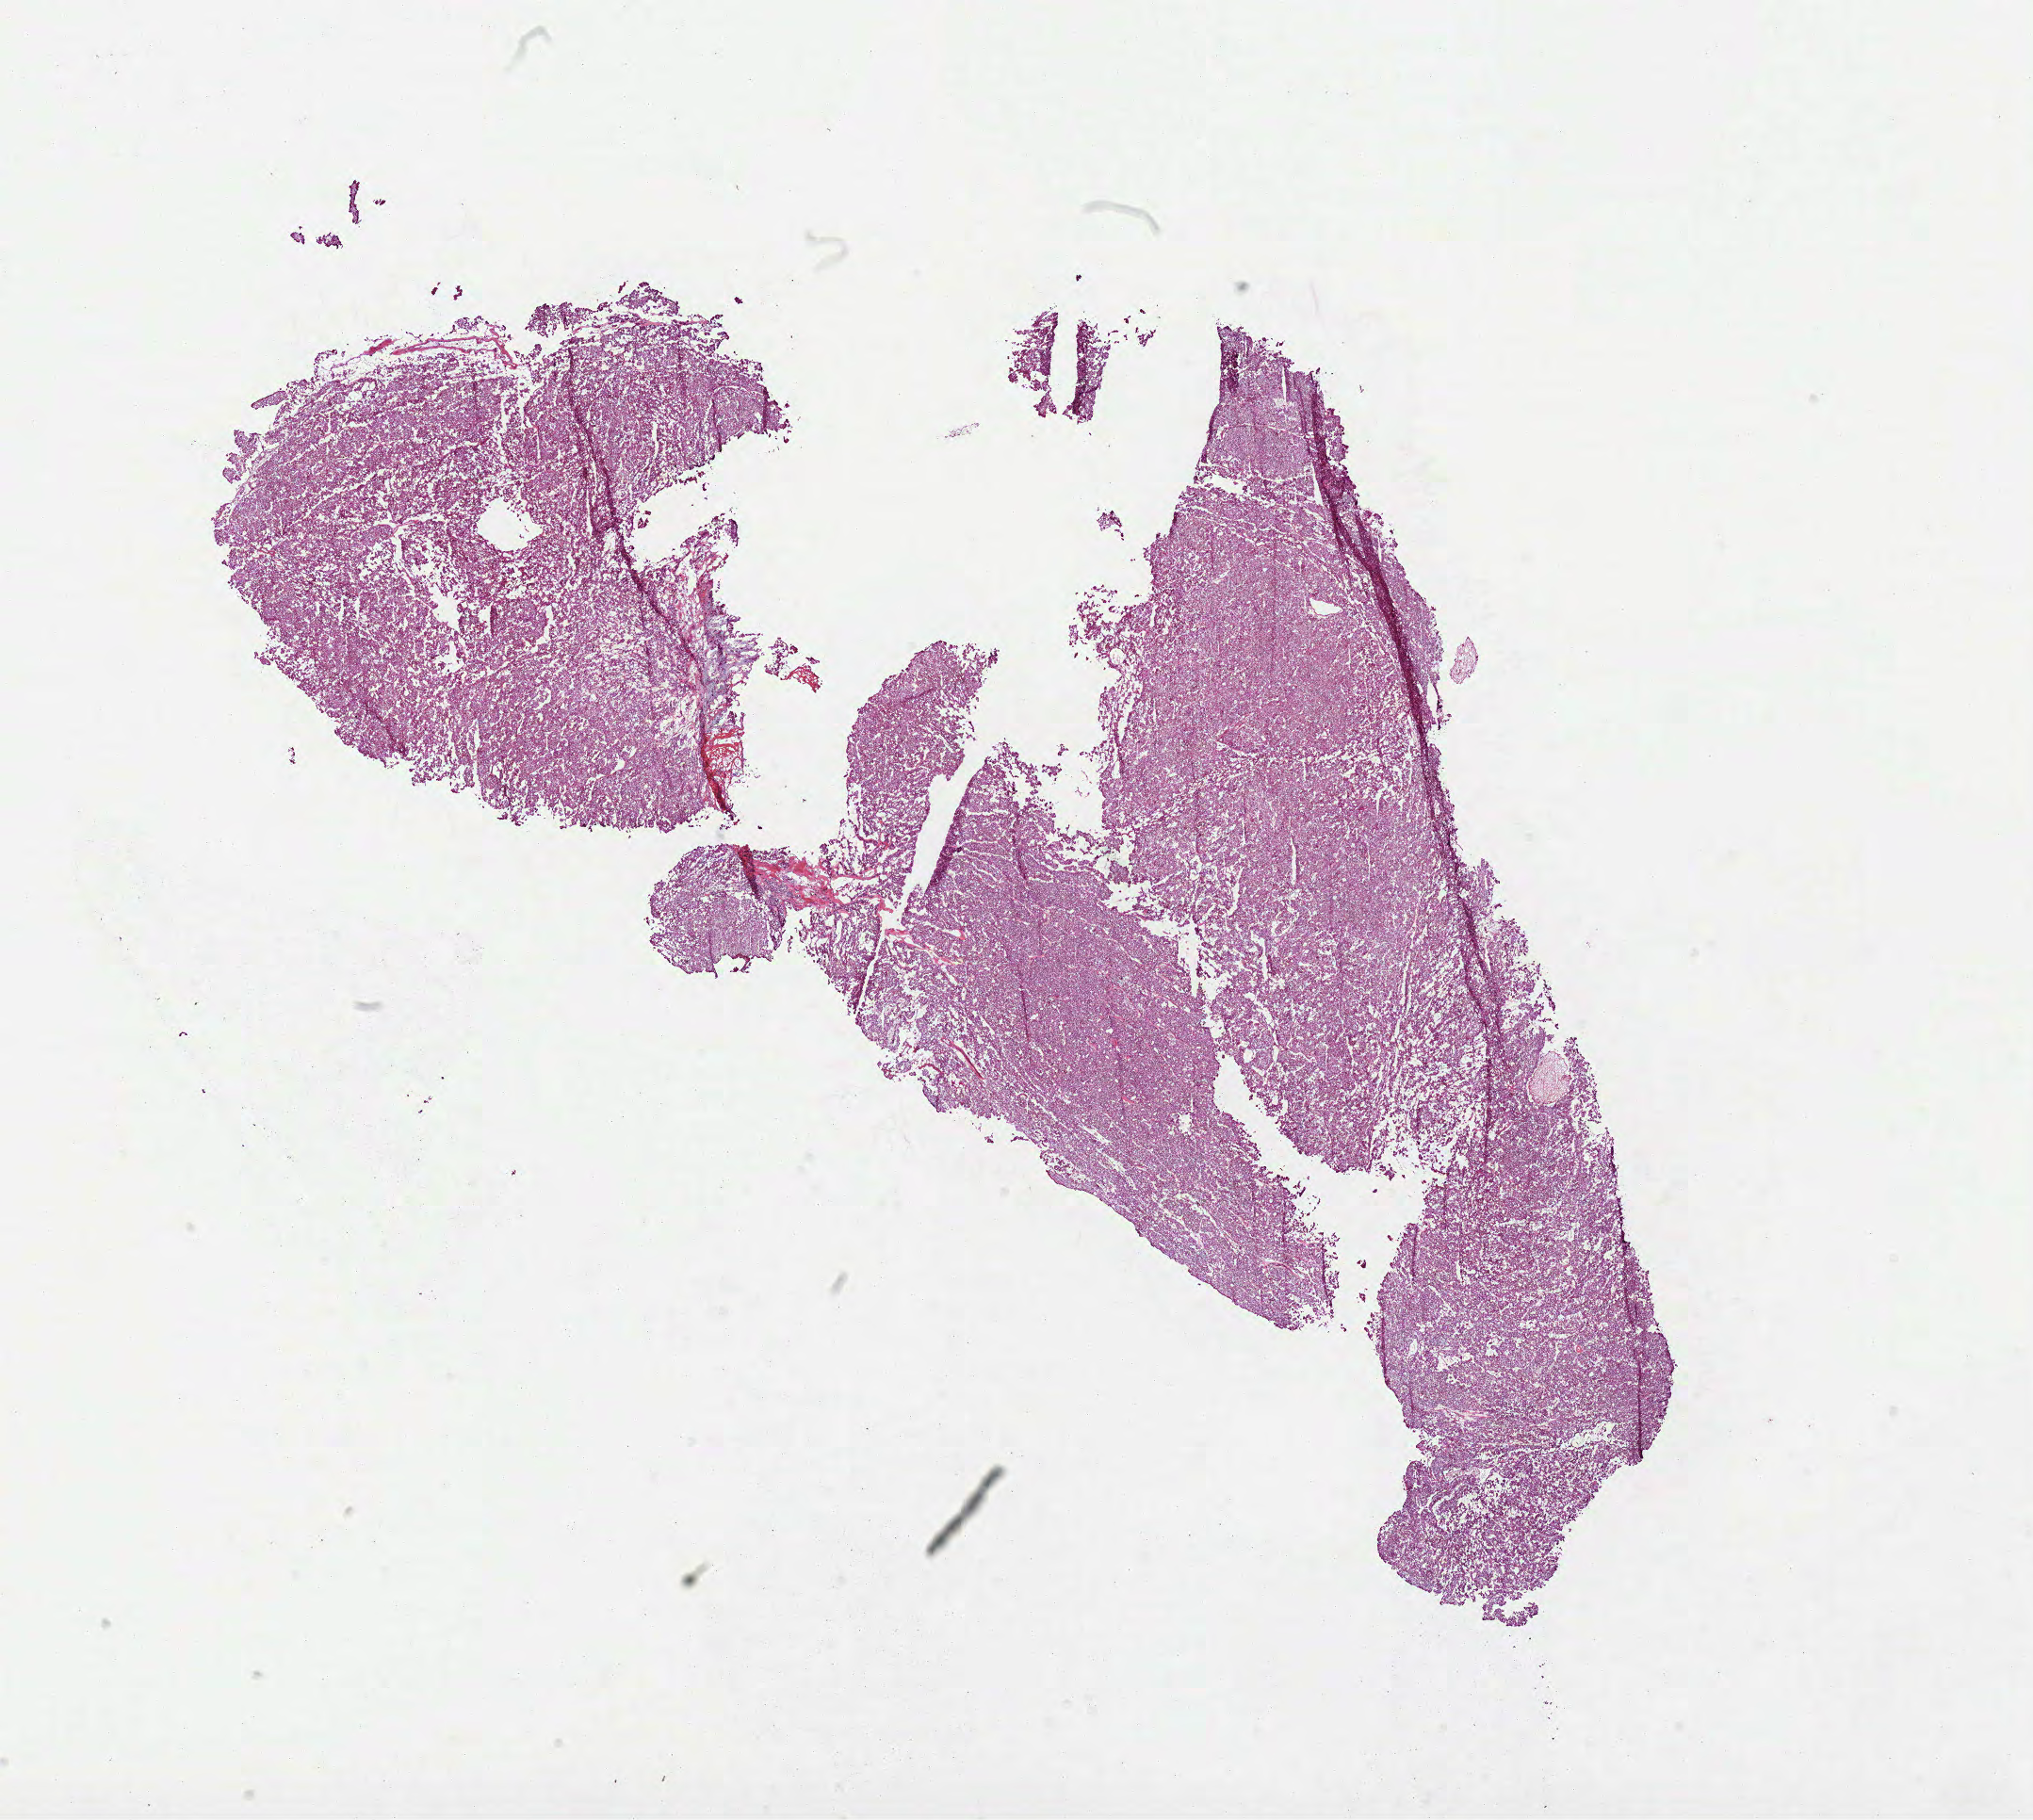
Whole-slide histology image, Hematoxylin and eosin (H&E) stained, whole scanned area (about 17.4 x 15.6 mm, acquisition: 40x scan) shown as a low-resolution overview. Frozen section. Sample: primary tumour, kidney. Male, age 75 years at initial diagnosis. Composition of this section per pathologist review: tumour cells 100%, tumour nuclei 95%, normal cells 0%, stromal cells 0%, necrosis 0%. Inflammatory infiltration, as recorded: lymphocyte infiltration 0%, monocyte infiltration 0%, neutrophil infiltration 0%.
Laterality: left. AJCC pathologic stage: I. Diagnosis: Renal cell carcinoma, chromophobe type.